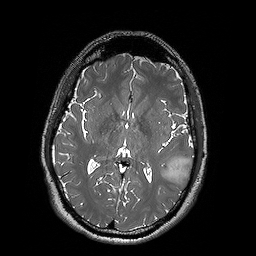
Brain MRI from a brain-tumour surgery series, one axial slice. Slice 88 of 192 in the series (ordered by position). 256 × 256 image matrix, field of view 250 × 250 mm. Case-level facts recorded for this patient, not image findings: histopathology: Oligodendroglioma; WHO grade: 2; IDH mutation: yes; tumour location: Left Posterior Temporal.
Annotated regions visible in this slice (outlined manually by an expert reader):
- tumour: bounding box (x1, y1, x2, y2) in pixels: (159, 156, 193, 180)